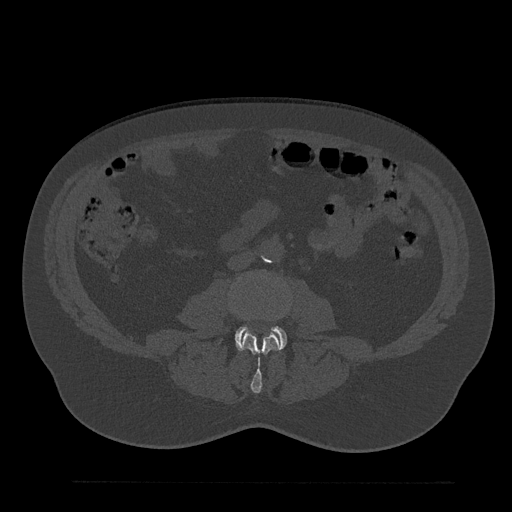
CT including the spine, one axial slice. Slice 3 of 797 in the series (ordered by position). 120 kVp. Bone window (W 1800 / L 400 HU). 0.5 mm slice thickness. 512 × 512 image matrix, field of view 430 × 430 mm. Male patient, age 61 years. Case-level facts recorded for this patient, not image findings: primary cancer: prostate.
Structures marked on this image (semi-automatically segmented with operator editing):
- L3 vertebra: bounding box <230,306,279,393> (left, top, right, bottom; pixels)
- L4 vertebra: <235,326,287,350>